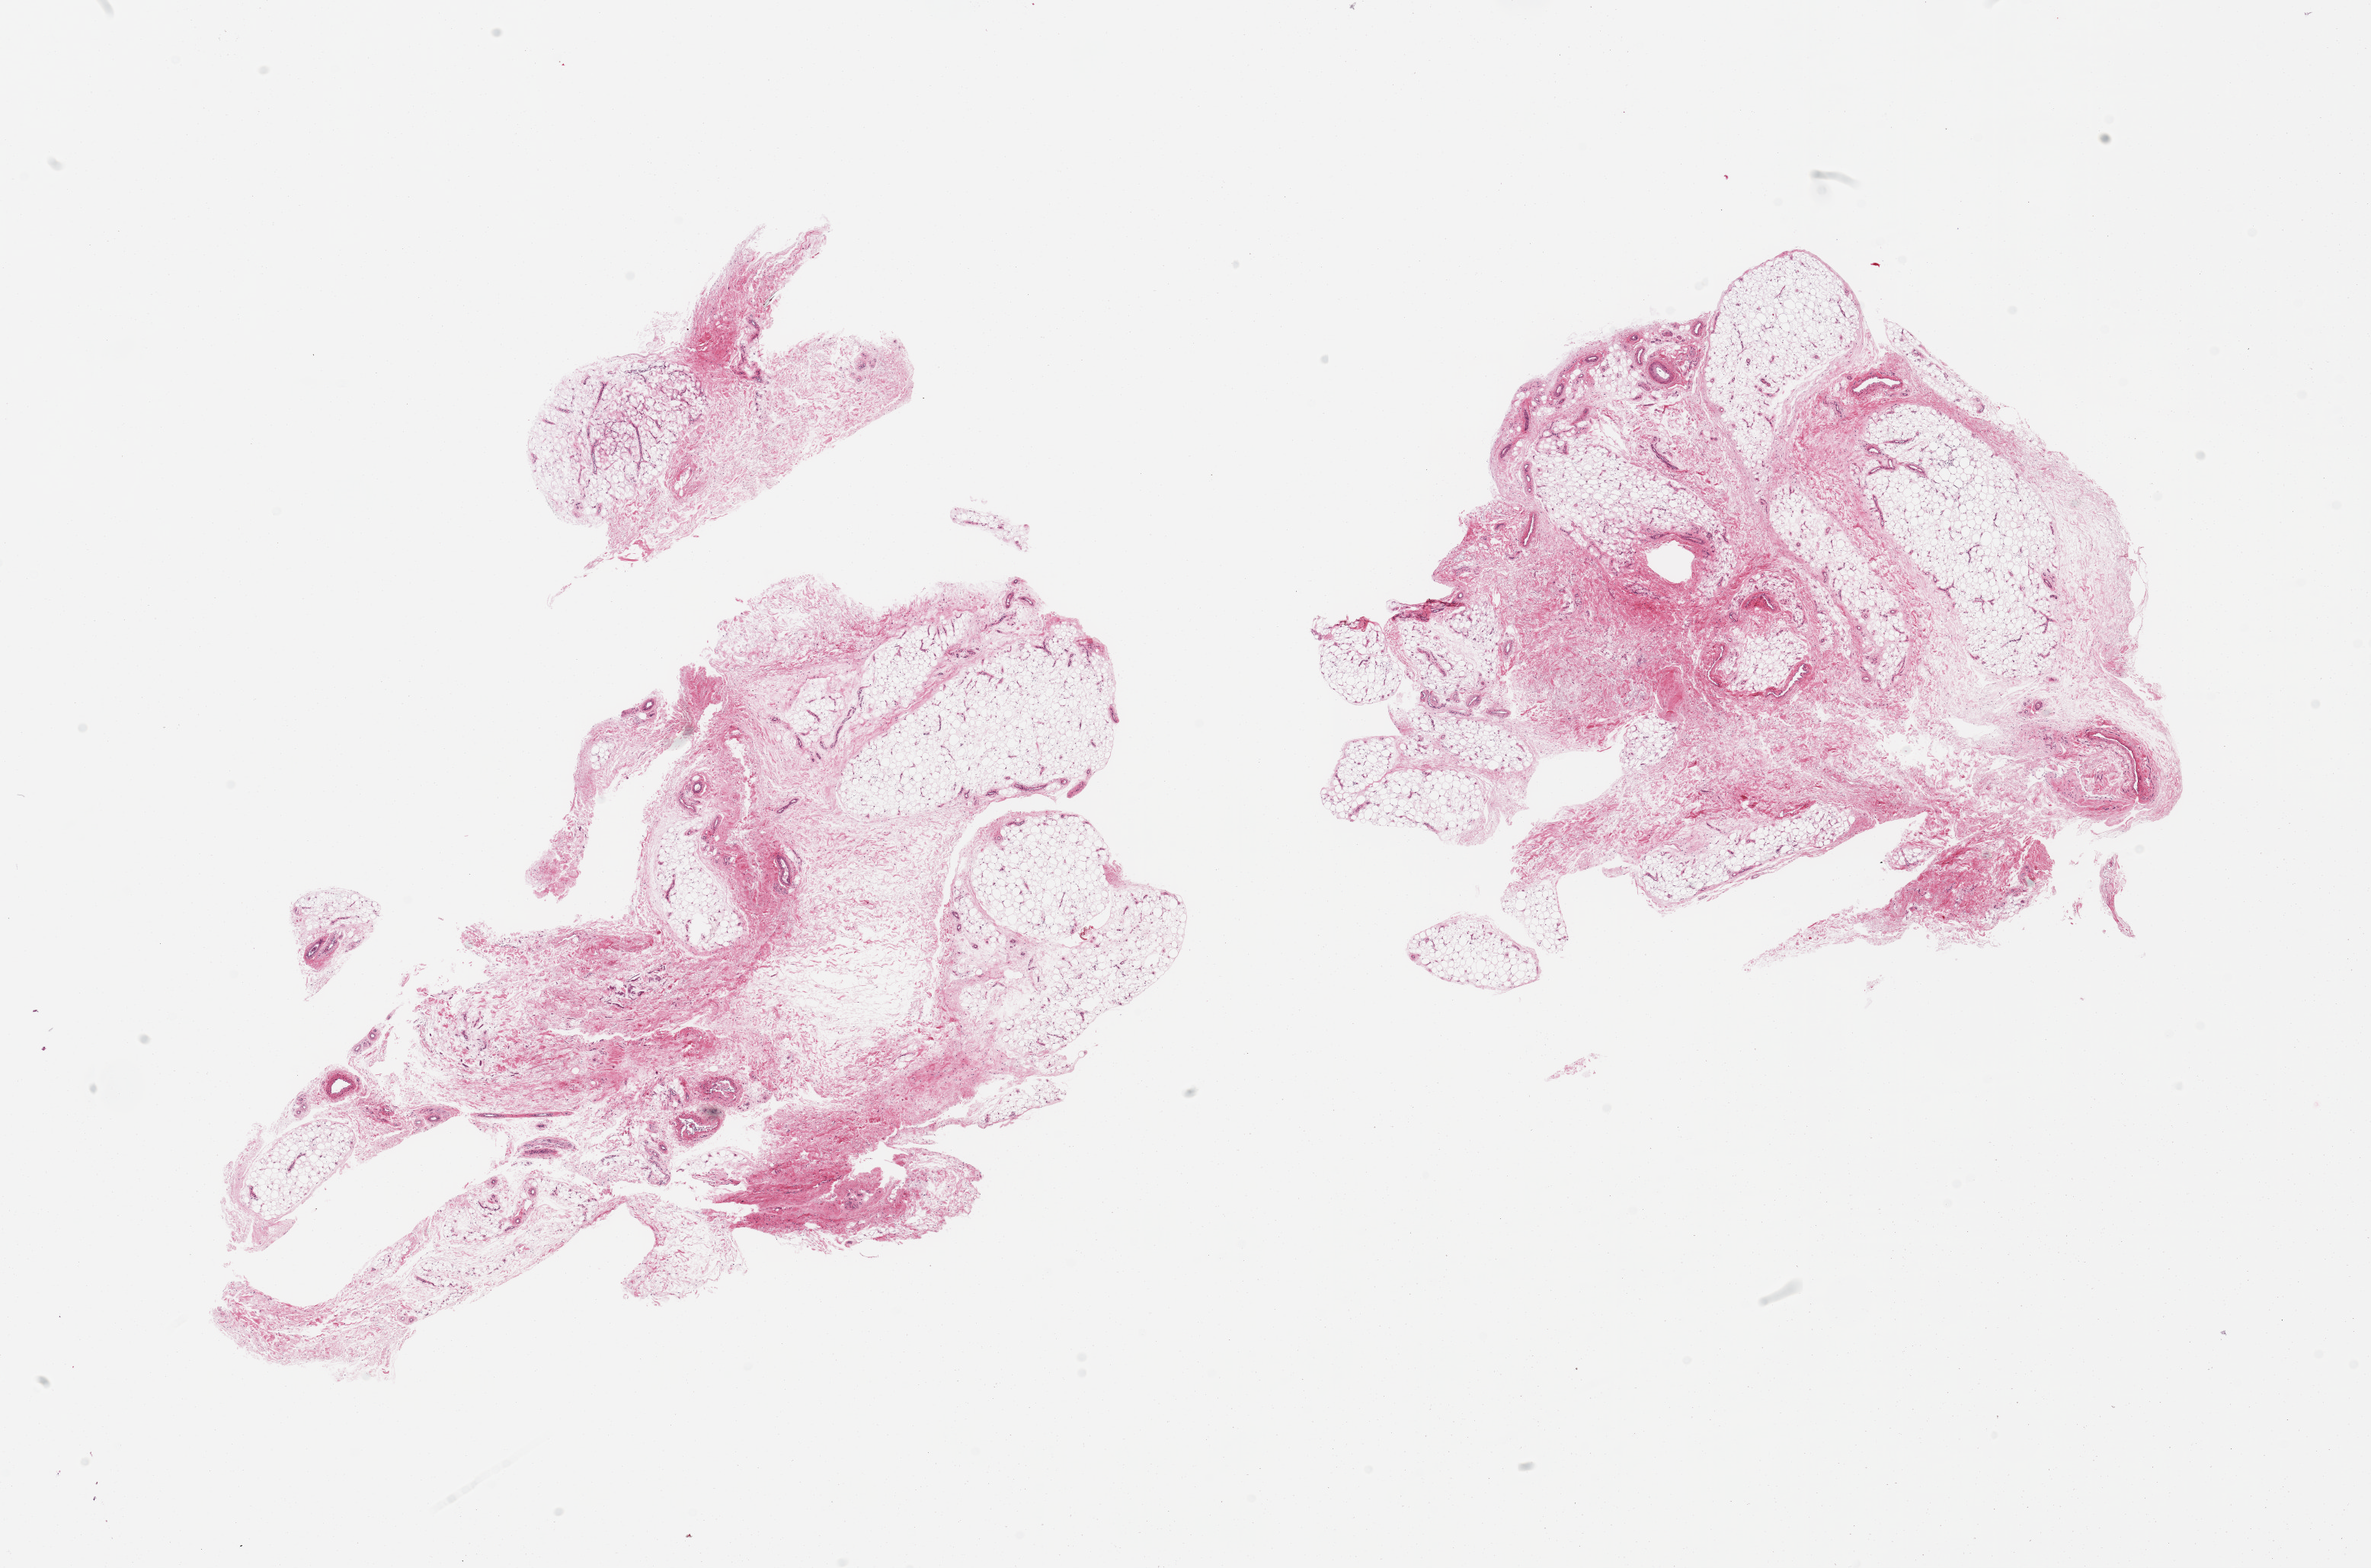
Haematoxylin and eosin whole-slide image — whole scanned area (about 24.6 x 16.3 mm) shown as a low-resolution overview, PAXgene-fixed paraffin-embedded (PFPE) section, section of adipose tissue (target tissue), donor tissue sample.
Reviewer comment on this tissue sample: 2 pieces; mature adipose tissue ~50% with fibrovascular component ~50%.